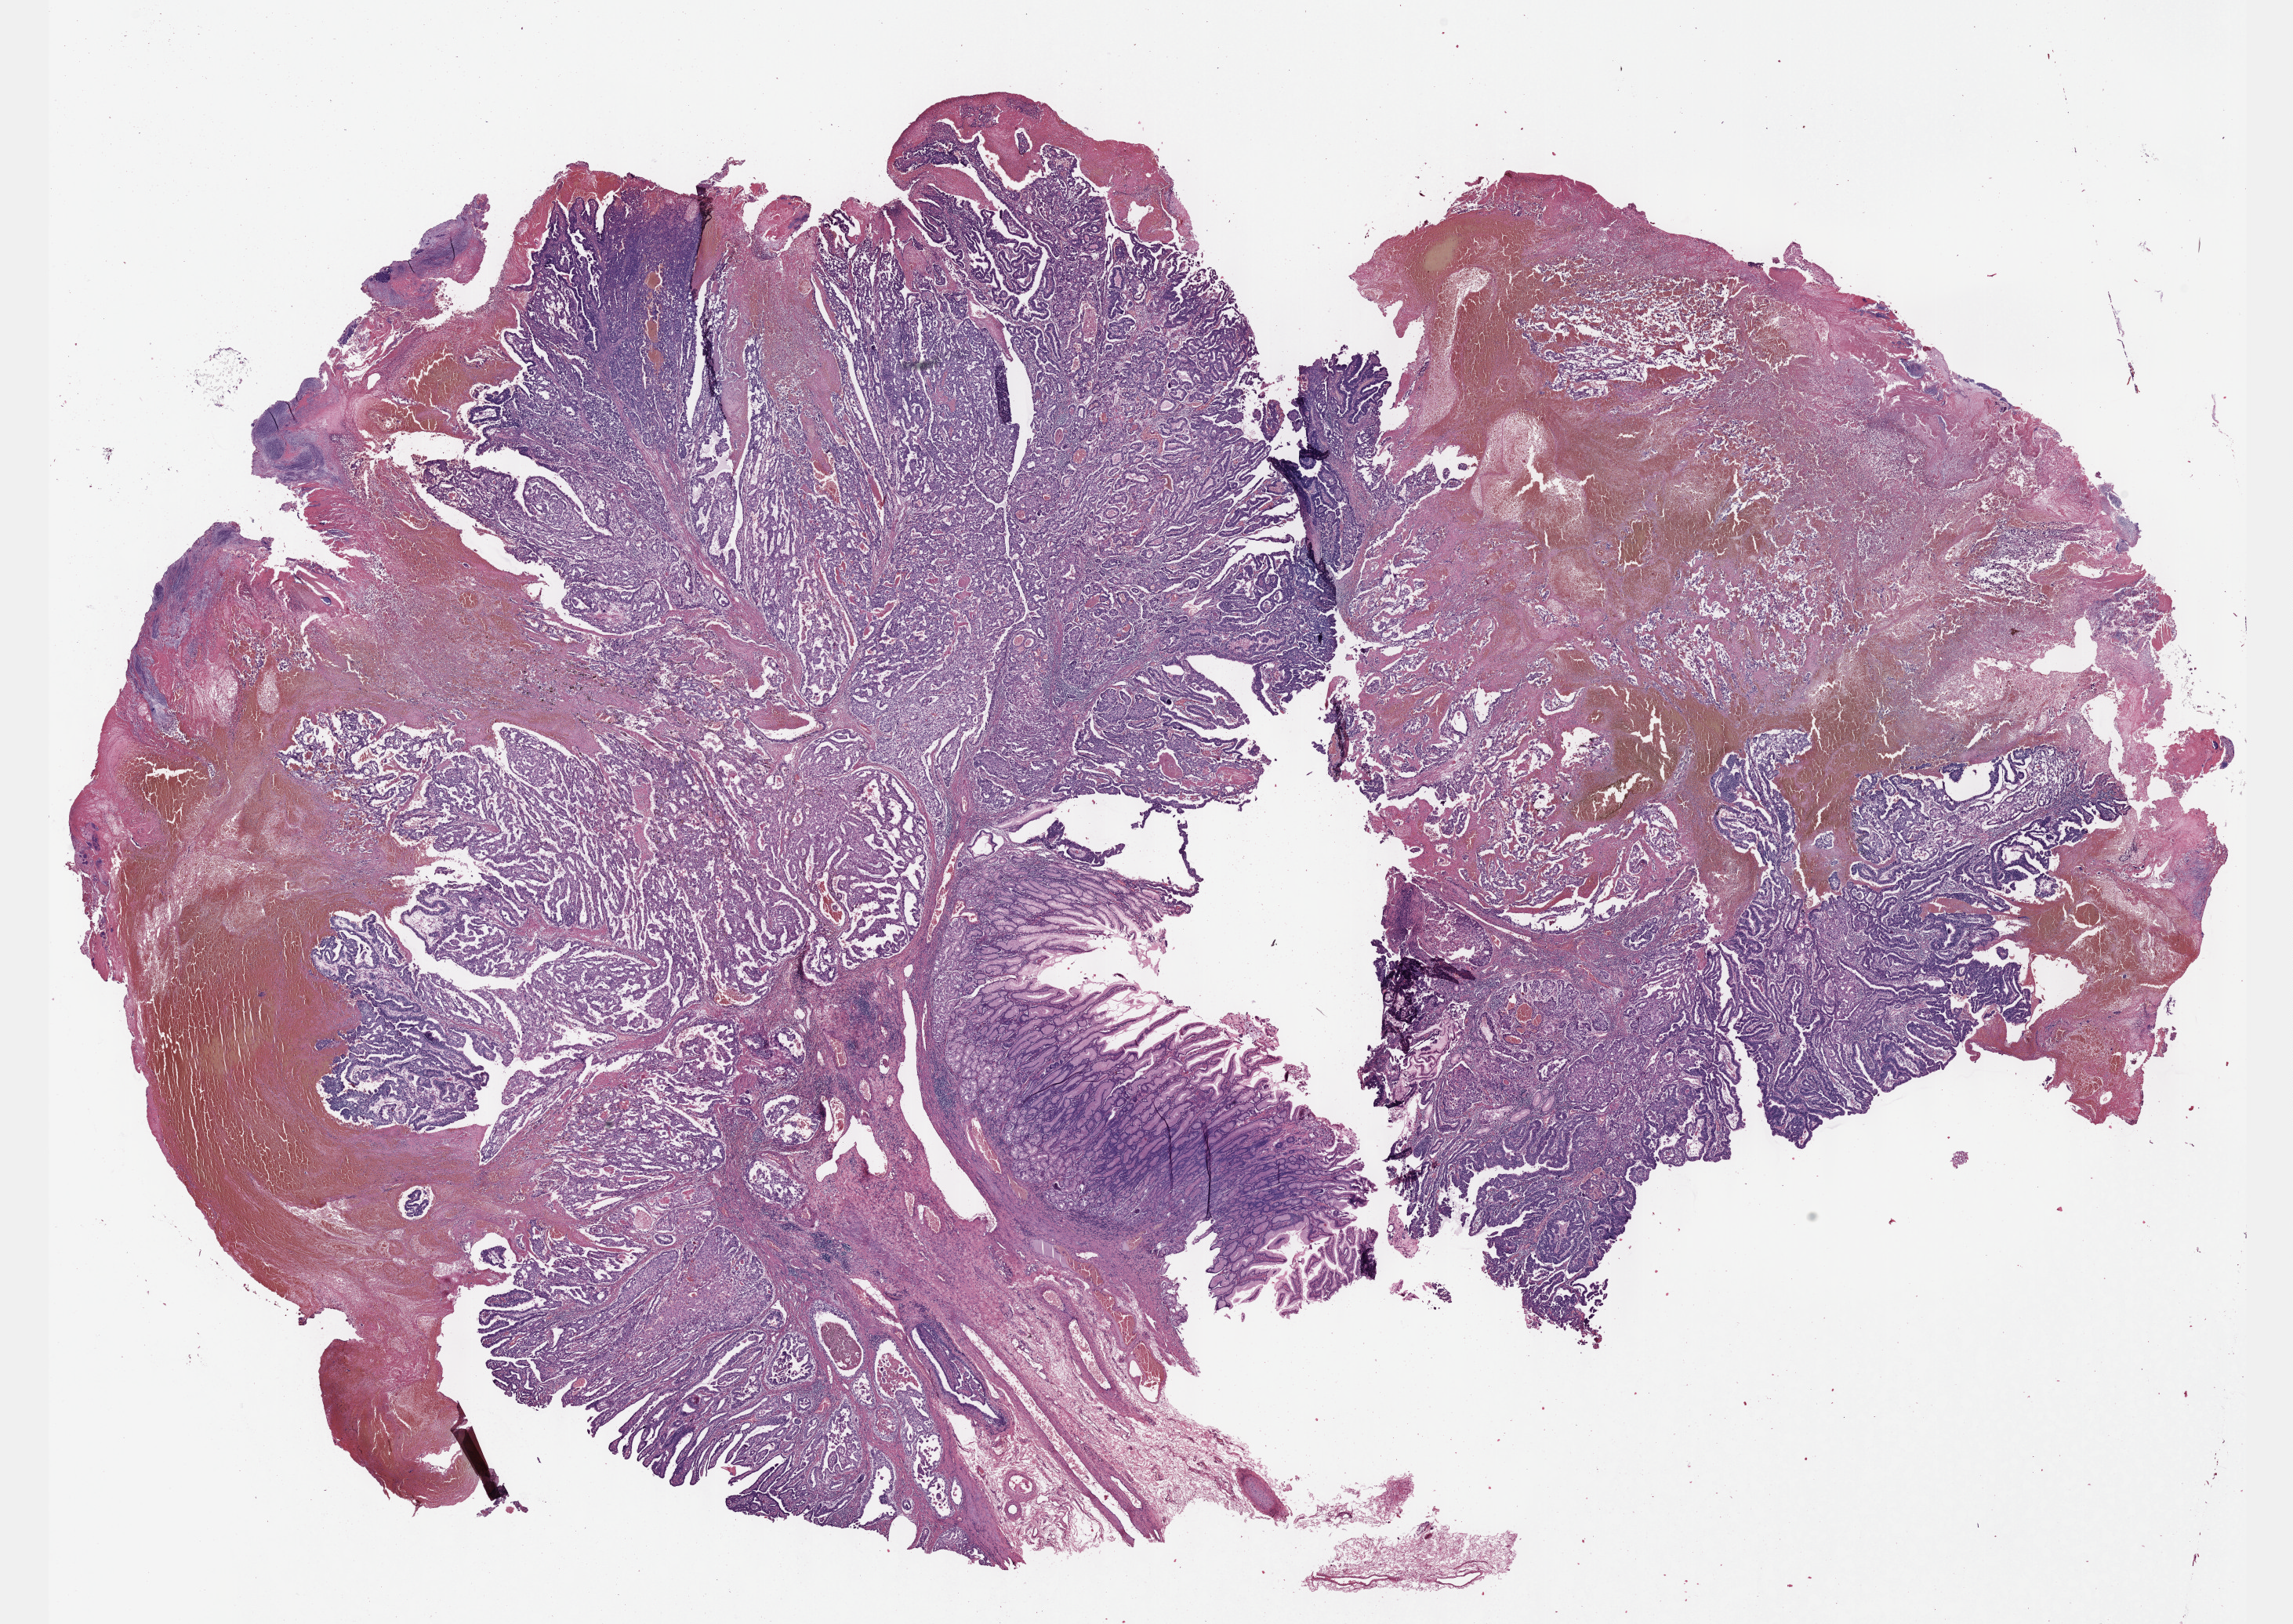
Digitized H&E-stained tissue section (whole slide), shown as a low-resolution overview of the whole scanned area (about 23.6 x 16.7 mm), formalin-fixed paraffin-embedded (FFPE) diagnostic section, sample: primary tumour, stomach. Male, age 48 years at initial diagnosis. Histologic grade: G2 (moderately differentiated).
- lymph nodes positive (case pathology): 0 of 16 examined
- histologic diagnosis: Adenocarcinoma, intestinal type
- TNM: T2 N0 M0
- AJCC pathologic stage: IB (6th edition)